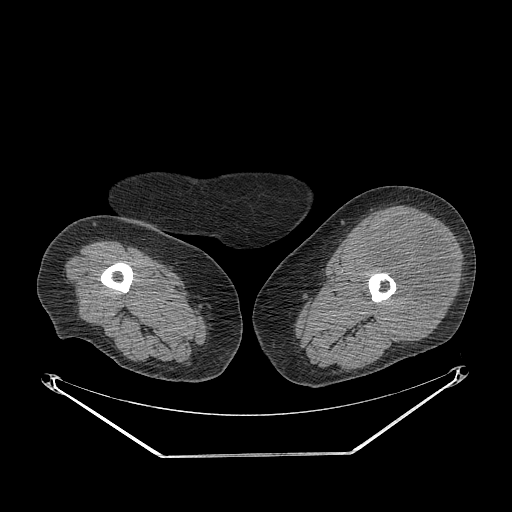
CT of an extremity soft-tissue mass (from a PET/CT study), one axial slice; position 224 of 267 along the scan axis; reconstruction kernel STANDARD; soft-tissue window (W 400 / L 40 HU); 3.75 mm slice thickness; 512 × 512 image matrix. Female patient. From the clinical record (not read from this slice): histological type: undifferentiated – high grade; grade: high; site of the primary tumour: left thigh.
Annotated regions visible in this slice (expert contour drawn on MRI and transferred to this co-registered scan by the dataset authors):
- gross tumour volume including surrounding oedema: box from (x=354, y=217) to (x=453, y=341) px
- gross tumour volume (mass): (x=354, y=217)–(x=453, y=341)